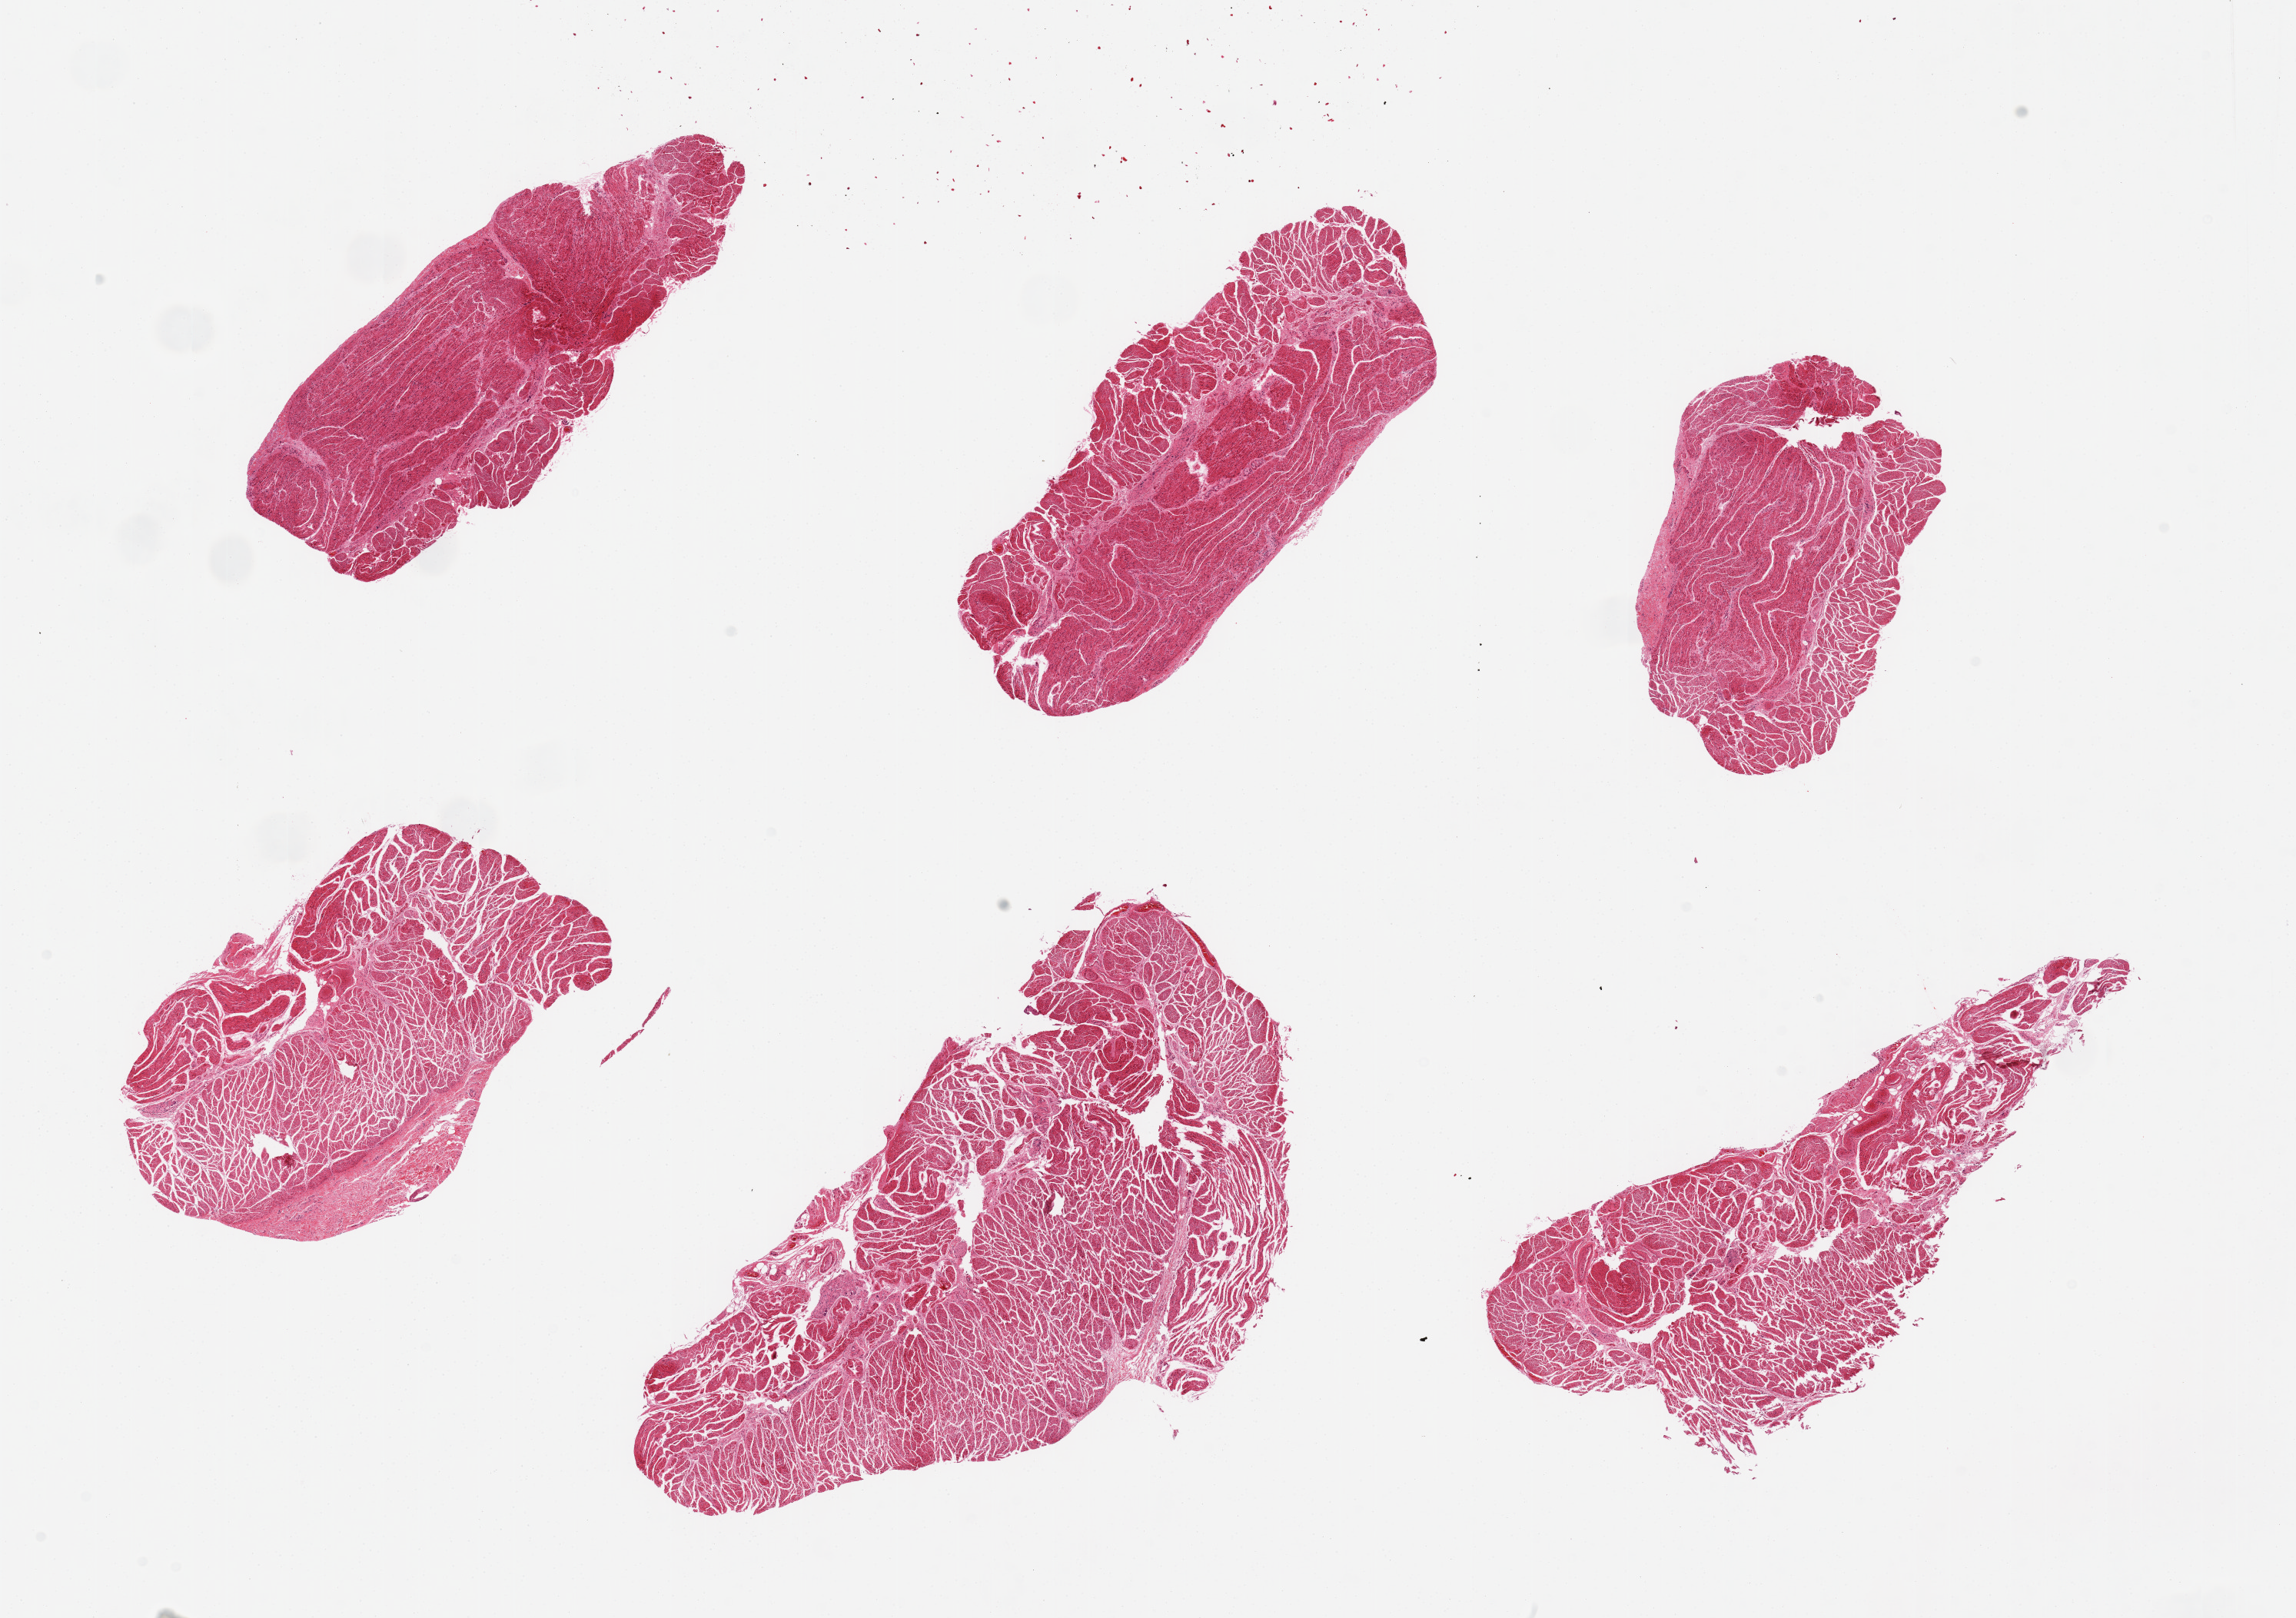
Hematoxylin and eosin (H&E) whole-slide image, brightfield — low-resolution overview of the scanned area, about 23.6 x 16.6 mm (acquisition: 20x scan). PAXgene-fixed, paraffin-embedded tissue. Target tissue: esophageal muscle. Tissue donor sample.
- pathologist's review note for this sample: 6 pieces, well trimmed